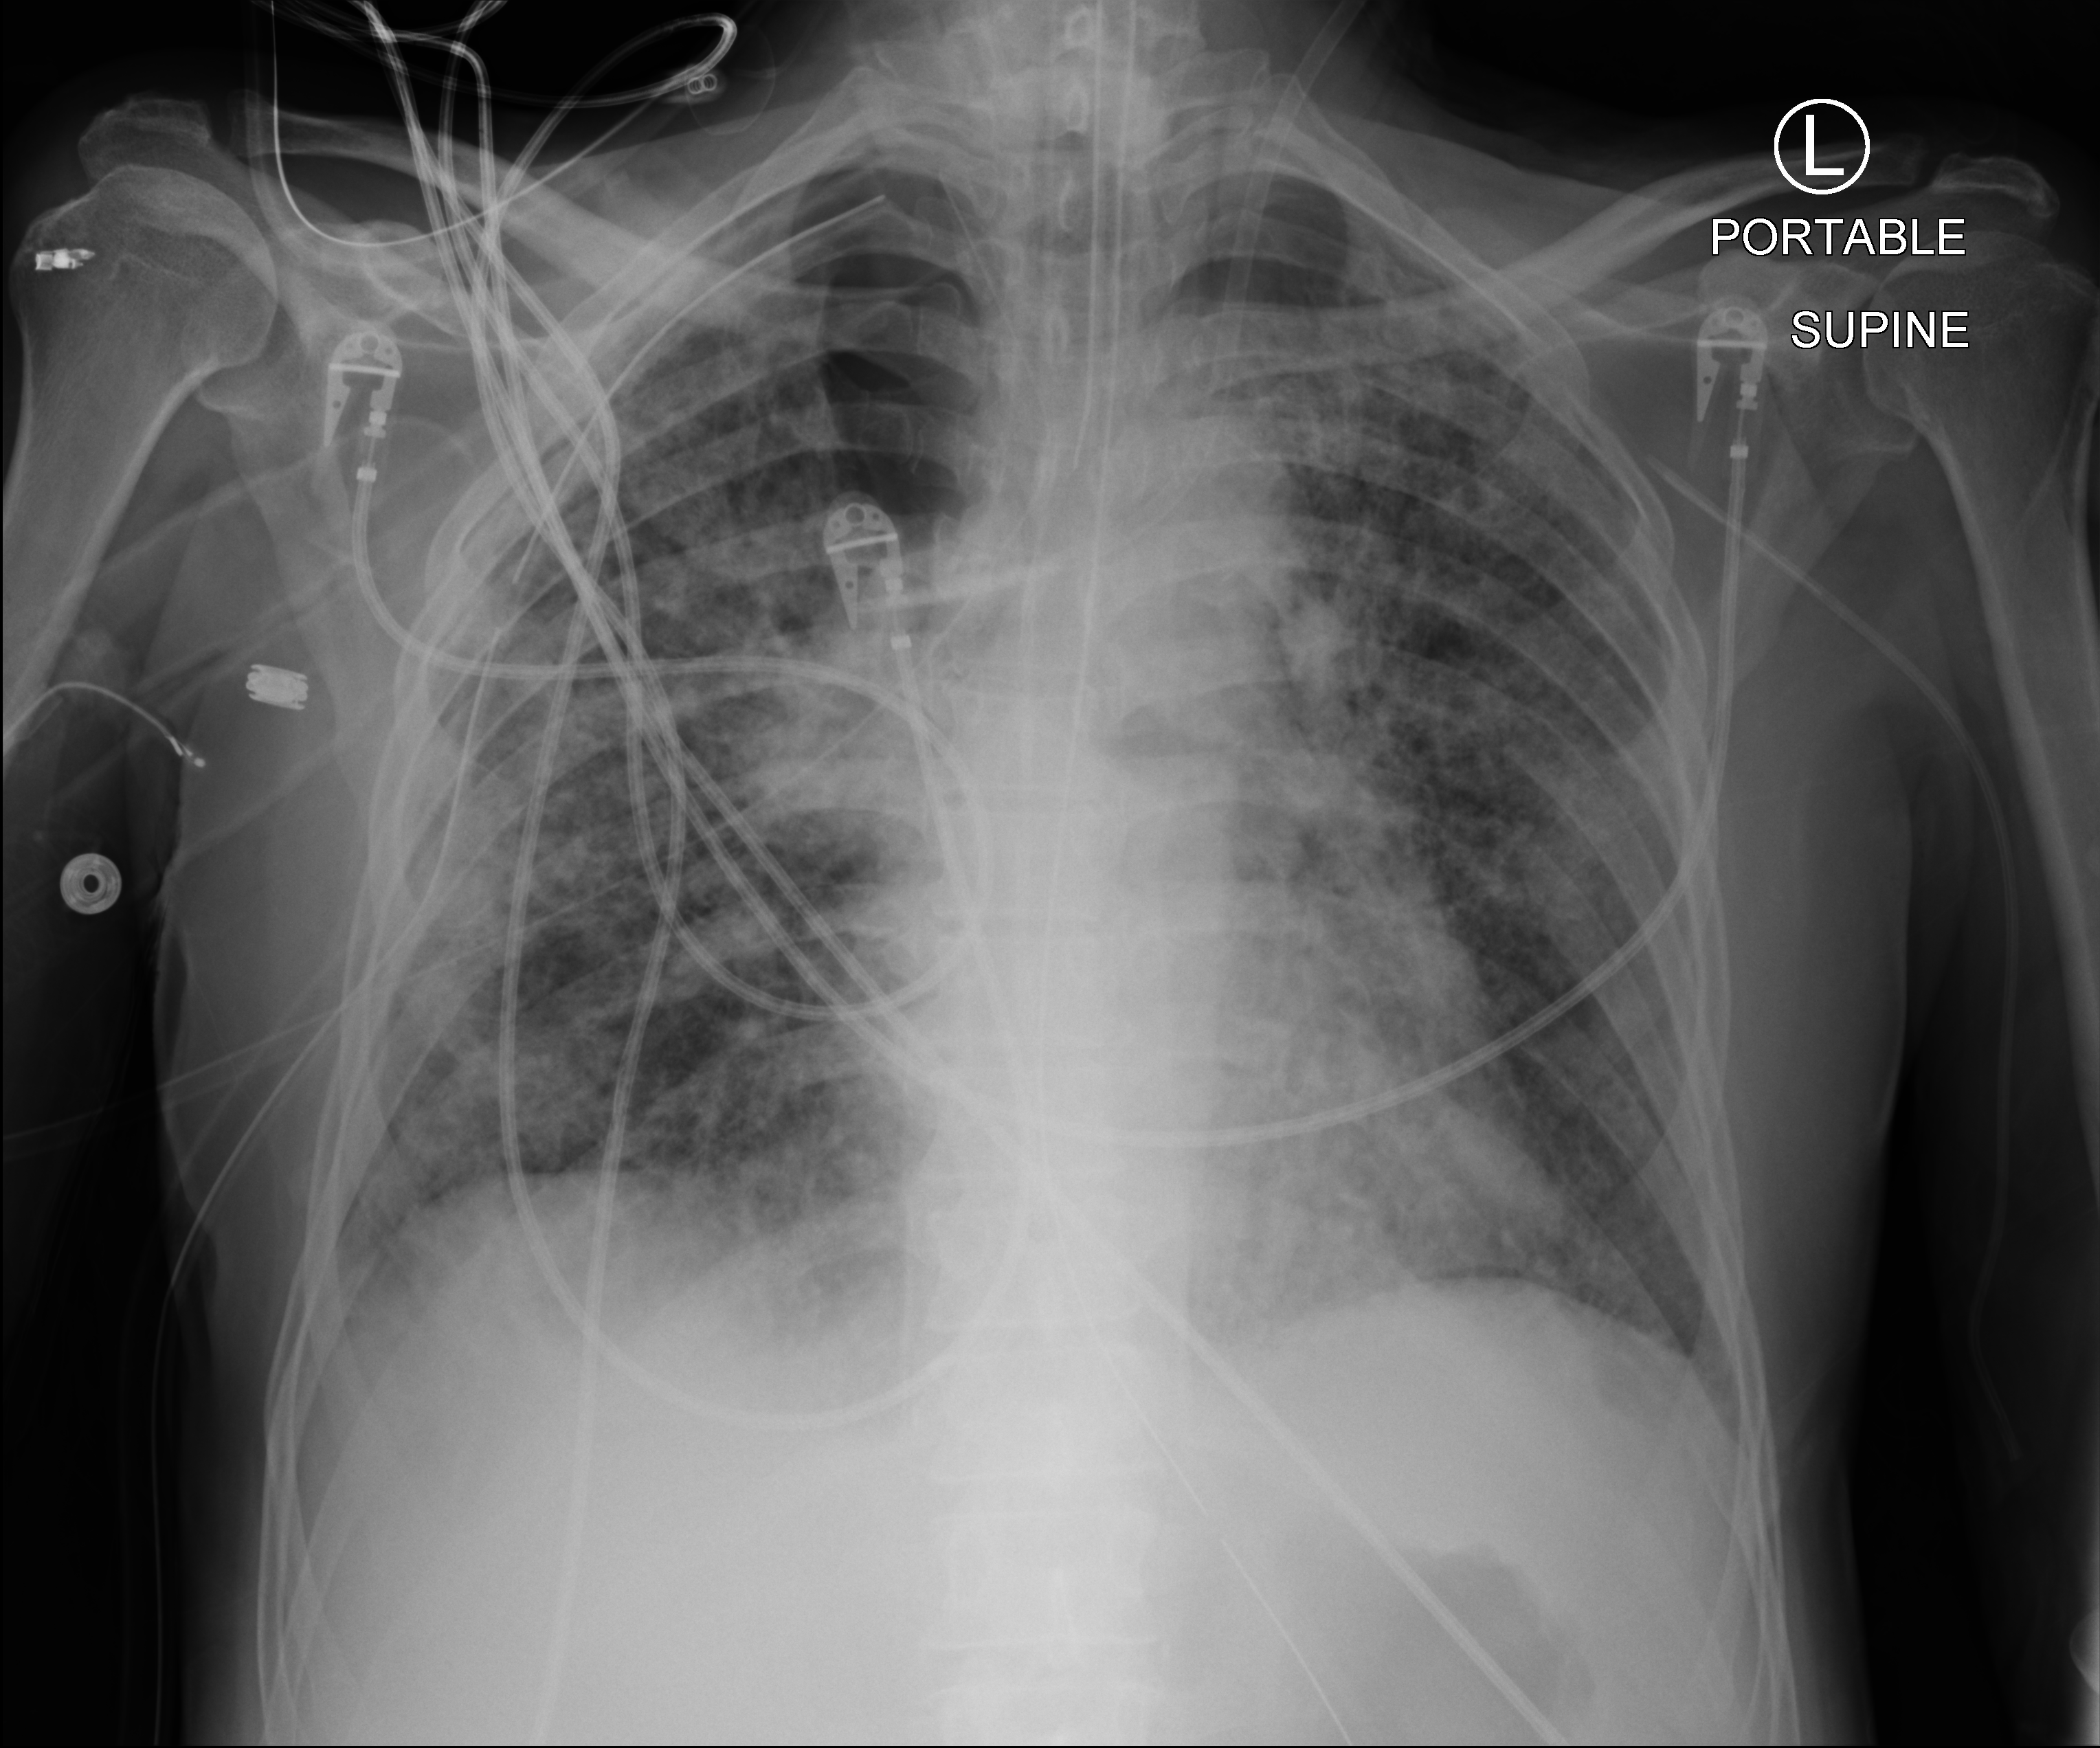
Bedside chest radiograph (computed radiography), anteroposterior (AP) projection. Patient hospitalised with COVID-19; male, aged 60–74 years.
From the hospital-stay record, not from the radiograph (when in the stay this image was taken is not recorded): mechanically ventilated during this hospital stay: yes; length of hospital stay: 65 days.